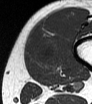
MRI of an extremity soft-tissue mass, one axial slice; slice 10 of 62 in the series (ordered by position); MR volume resampled by the dataset authors to the PET/CT grid (not the native acquisition matrix); 3.27 mm slice thickness; 92 × 104 image matrix, field of view 90 × 102 mm. Male patient. Case-level facts recorded for this patient, not image findings: histological type: mixoid liposarcoma; grade: low; site of the primary tumour: left thigh.
Outlined on this slice (expert contour drawn on MRI and transferred to this co-registered scan by the dataset authors):
- gross tumour volume (mass): bounding box (x1, y1, x2, y2) in pixels: (39, 45, 56, 61)